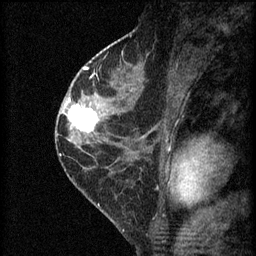
Breast MRI (dynamic contrast-enhanced), one sagittal slice. Position 33 of 60 along the scan axis. 3 images stored at this slice position (order not interpretable as contrast timing). 1.5 T. TE 4.2 ms, TR 8.2 ms. 256 × 256 image matrix, field of view 180 × 180 mm. Female patient, age 45 years.
Outlined on this slice (semi-automatically segmented with operator editing):
- analysis volume of interest (the breast-tissue region the enhancement analysis was run in; not a lesion): box from (x=62, y=98) to (x=104, y=139) px
- tumour enhancement mask (voxels above the 70 % enhancement threshold inside the analysis volume of interest): (x=66, y=98)–(x=100, y=133)